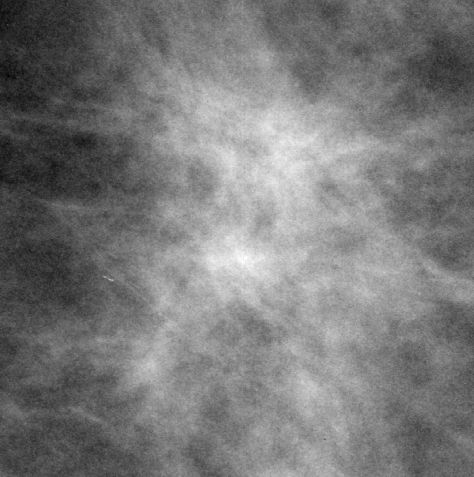
Crop from a digitized film mammogram around one marked abnormality; left breast; CC view; BI-RADS breast density category 1 (scale 1–4).
Finding: mass, shape architectural distortion; BI-RADS assessment category 3; benign; no additional work-up was recommended (benign without callback).